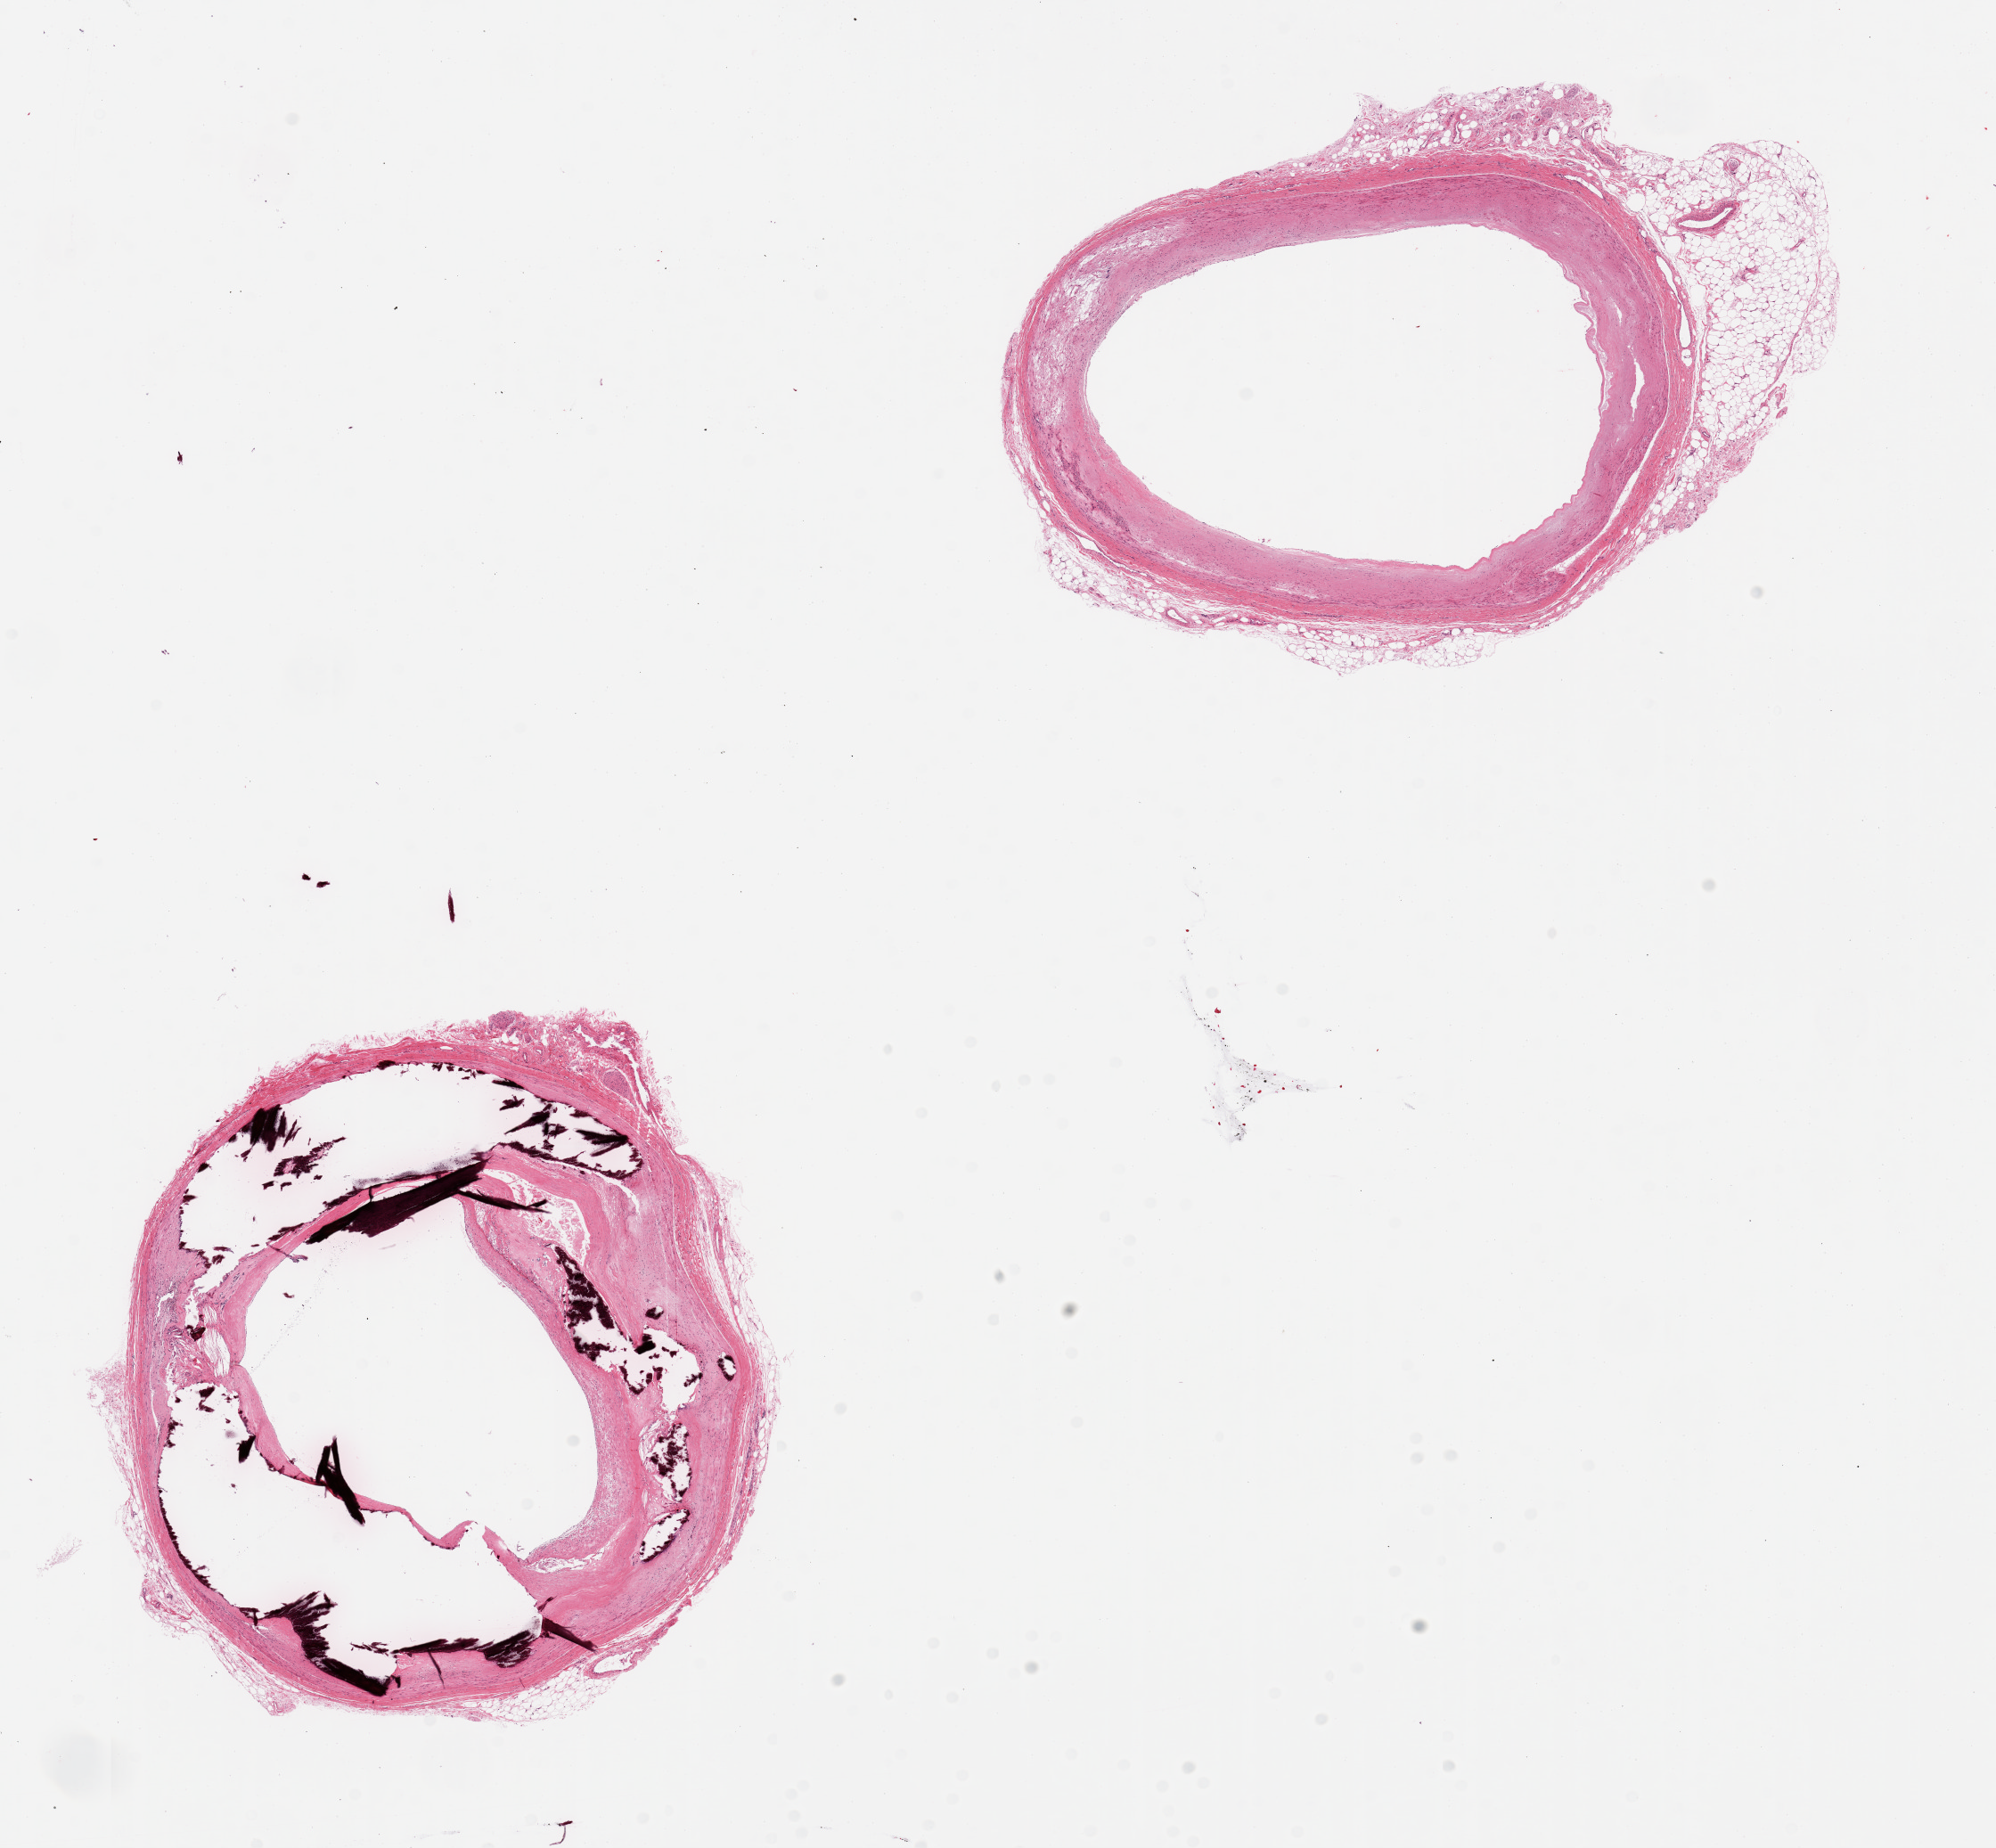
Haematoxylin and eosin whole-slide image, shown as a low-resolution overview of the whole scanned area (about 17.7 x 16.4 mm, from a 20x scan), PAXgene-fixed paraffin-embedded (PFPE) section, target tissue: coronary artery, donor tissue sample. Donor sex: male.
• review note (as recorded): 2 pieces; 1 with 50% narrowing by calcific deposits; other has 3x1mm adherent fat